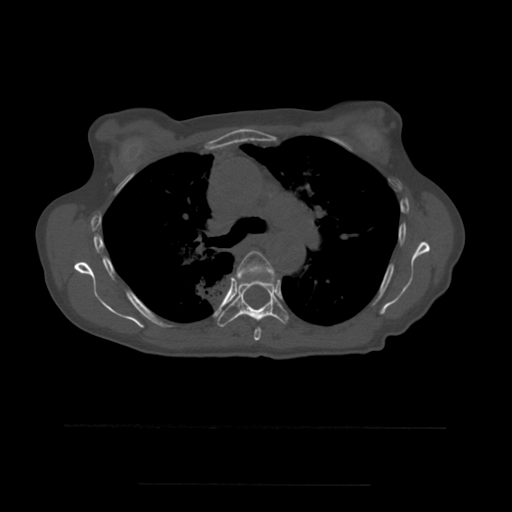
CT including the spine, one axial slice; position 381 of 544 along the scan axis; bone window (W 1800 / L 400 HU); 1.25 mm slice thickness; 512 × 512 image matrix, field of view 350 × 350 mm. Patient age 58 years. Case-level facts recorded for this patient, not image findings: primary cancer: lung.
Outlined on this slice (semi-automatically segmented with operator editing):
- T5 vertebra: bounding box [x1, y1, x2, y2] px = [236, 251, 276, 341]
- T6 vertebra: [218, 278, 289, 327]